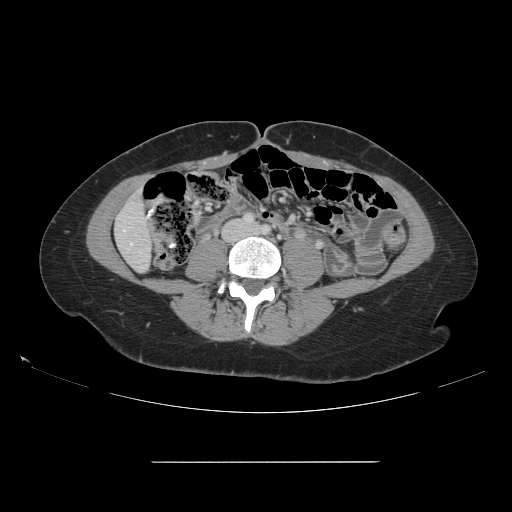
Contrast-enhanced abdominal CT, one axial slice; slice 21 of 151 in the series (ordered by position); intravenous contrast given; soft-tissue window (W 400 / L 40 HU); 2.5 mm slice thickness; 512 × 512 image matrix. Female patient, age 46 years. From the clinical record (not read from this slice): diagnosis: colorectal cancer liver metastases, imaged before liver resection; multiple liver metastases: yes; largest metastasis: 3 cm; disease in both lobes: yes.
Annotated regions visible in this slice (outlined manually by an expert reader):
- liver: bounding box [x1, y1, x2, y2] px = [116, 193, 151, 271]
- planned liver remnant (the part of the liver to remain after resection): [116, 193, 151, 271]